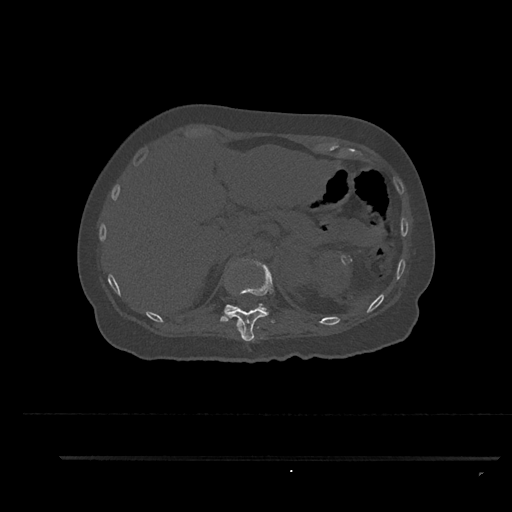
CT including the spine, one axial slice; position 297 of 797 along the scan axis; reconstruction kernel Br40s/3; 120 kVp; bone window (W 1800 / L 400 HU); 0.5 mm slice thickness; 512 × 512 image matrix, field of view 408 × 408 mm. Female patient, age 44 years. Case-level facts recorded for this patient, not image findings: primary cancer: renal; vertebrae with lytic lesions (as recorded): L1.
Outlined on this slice (semi-automatically segmented with operator editing):
- T11 vertebra: bounding box <228,260,274,342> (left, top, right, bottom; pixels)
- T12 vertebra: <220,303,269,322>